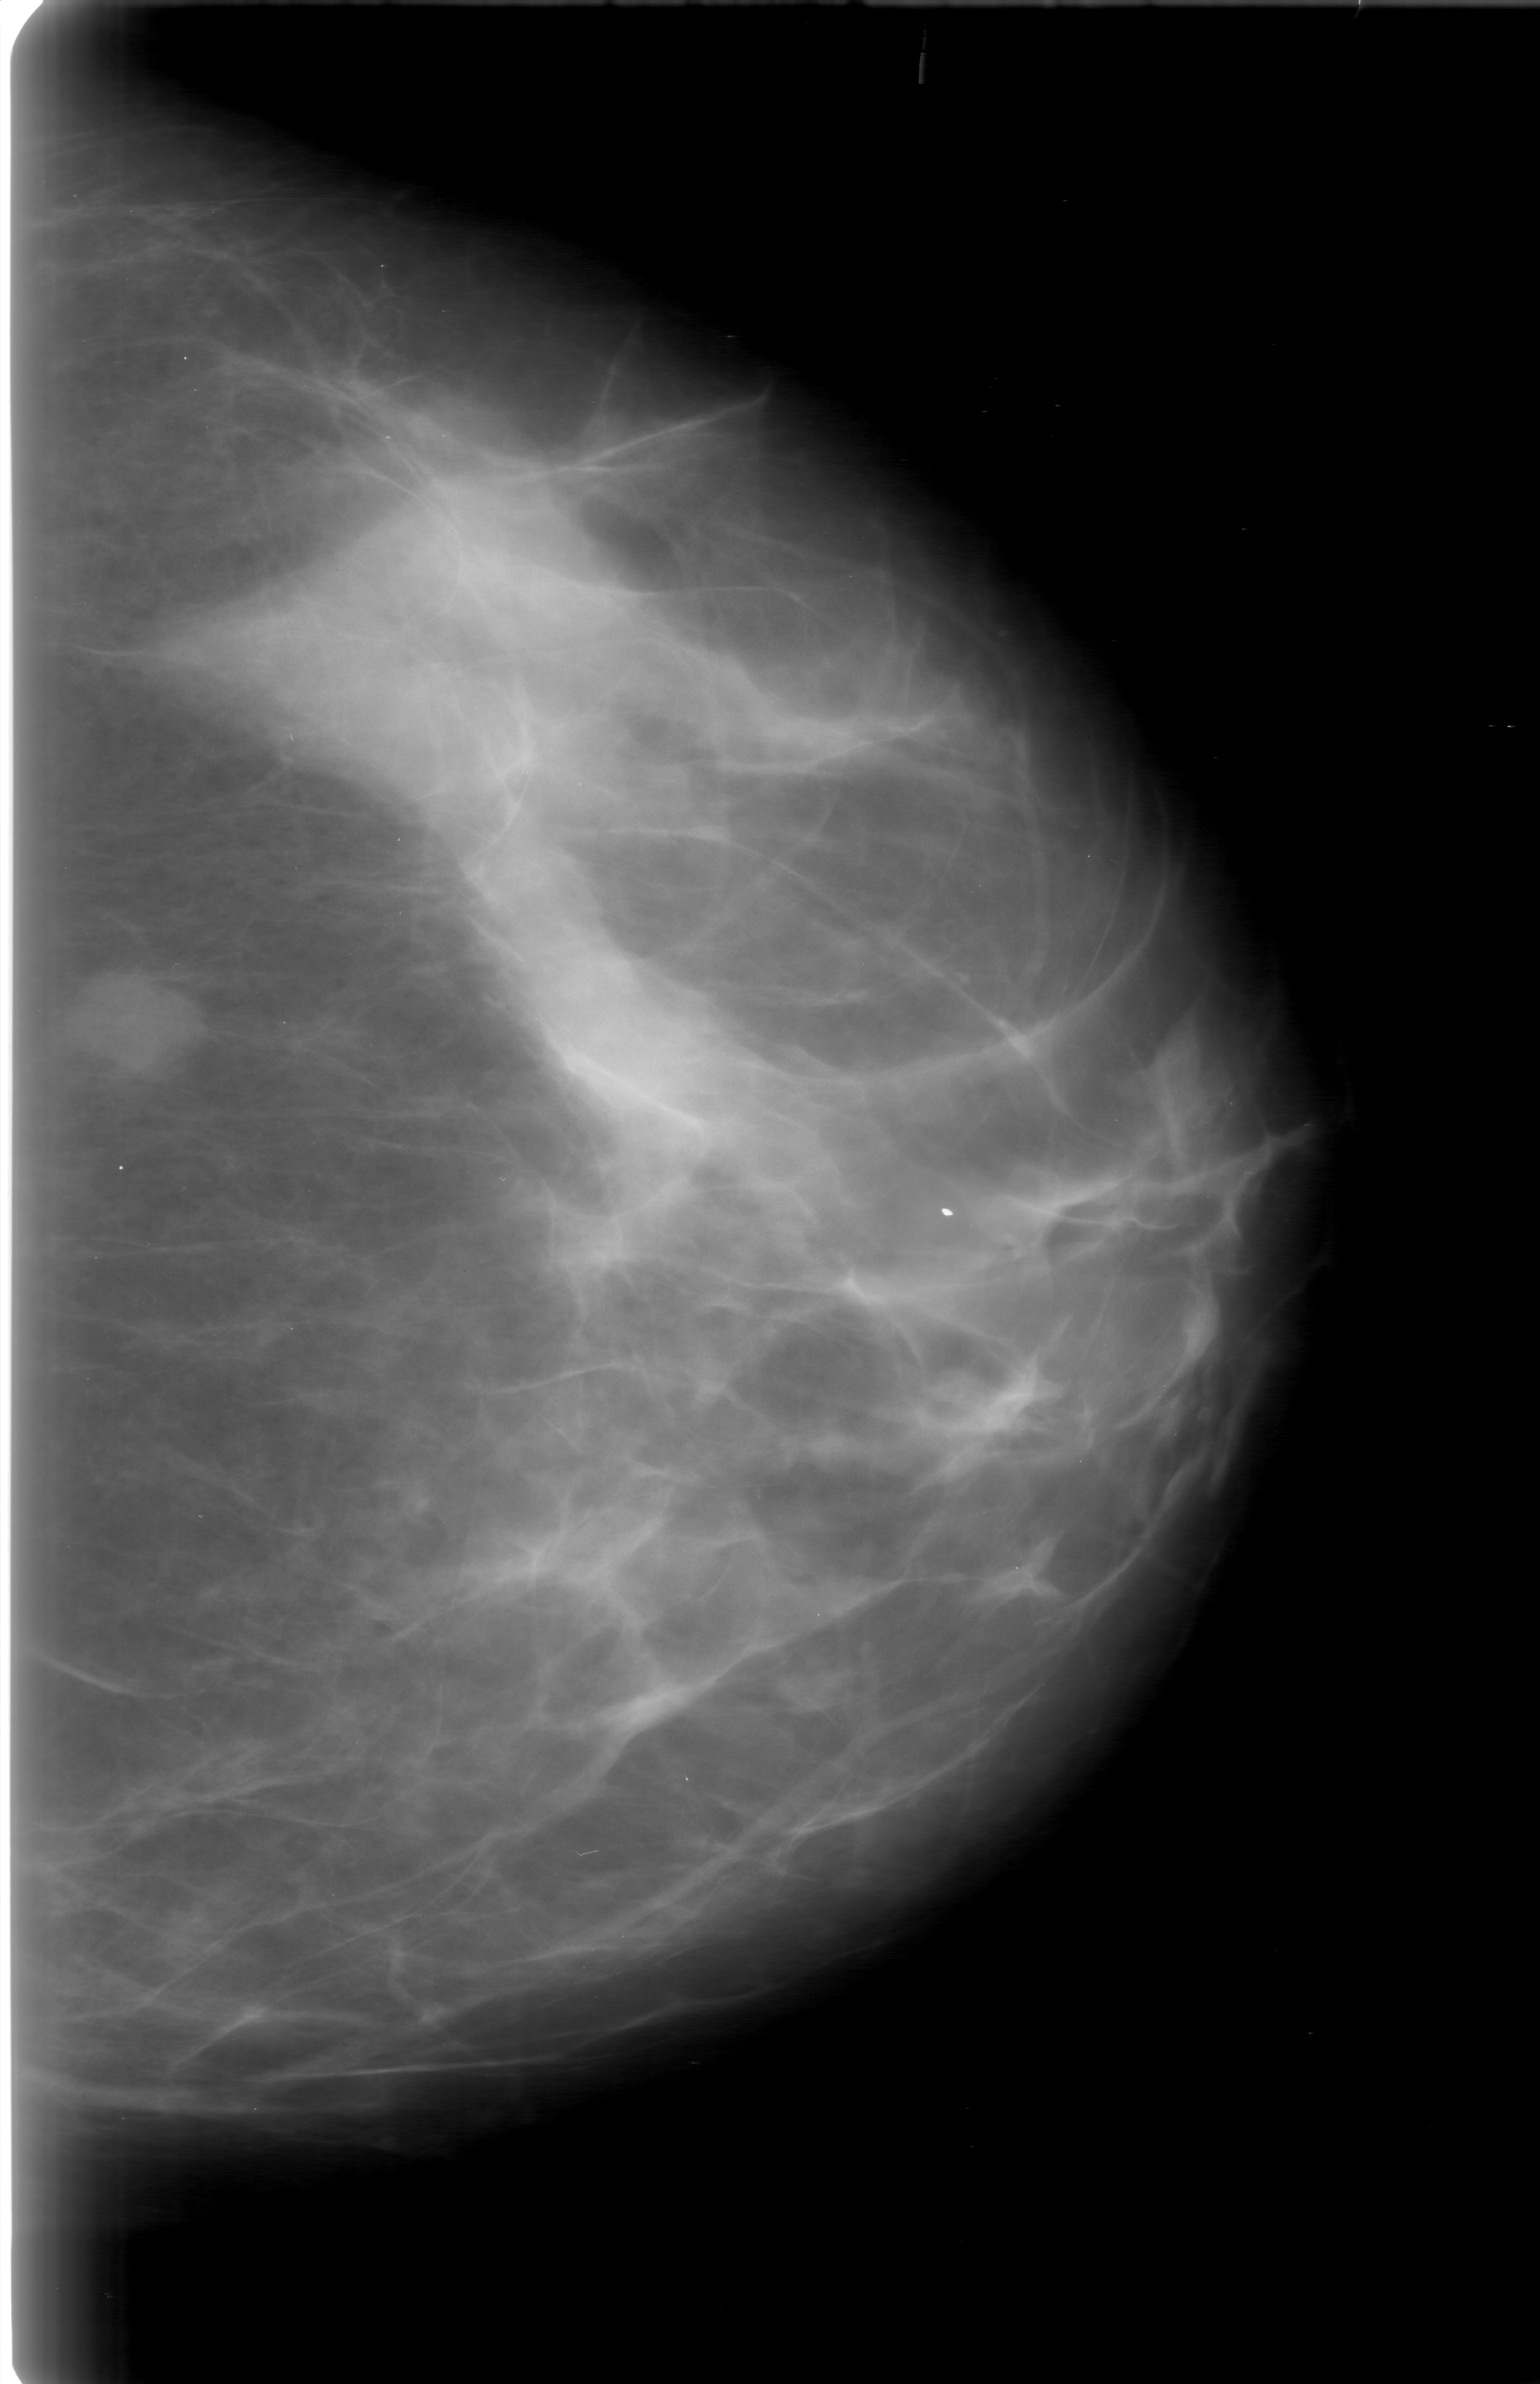
Mammogram (digitized film). Left breast. CC view. 1540 × 2384 image matrix.
Expert-marked regions of interest on this image (one box per marked abnormality):
- mass, shape oval, margins obscured; BI-RADS assessment category 0; pathology (as recorded): benign: box from (x=98, y=955) to (x=239, y=1096) px